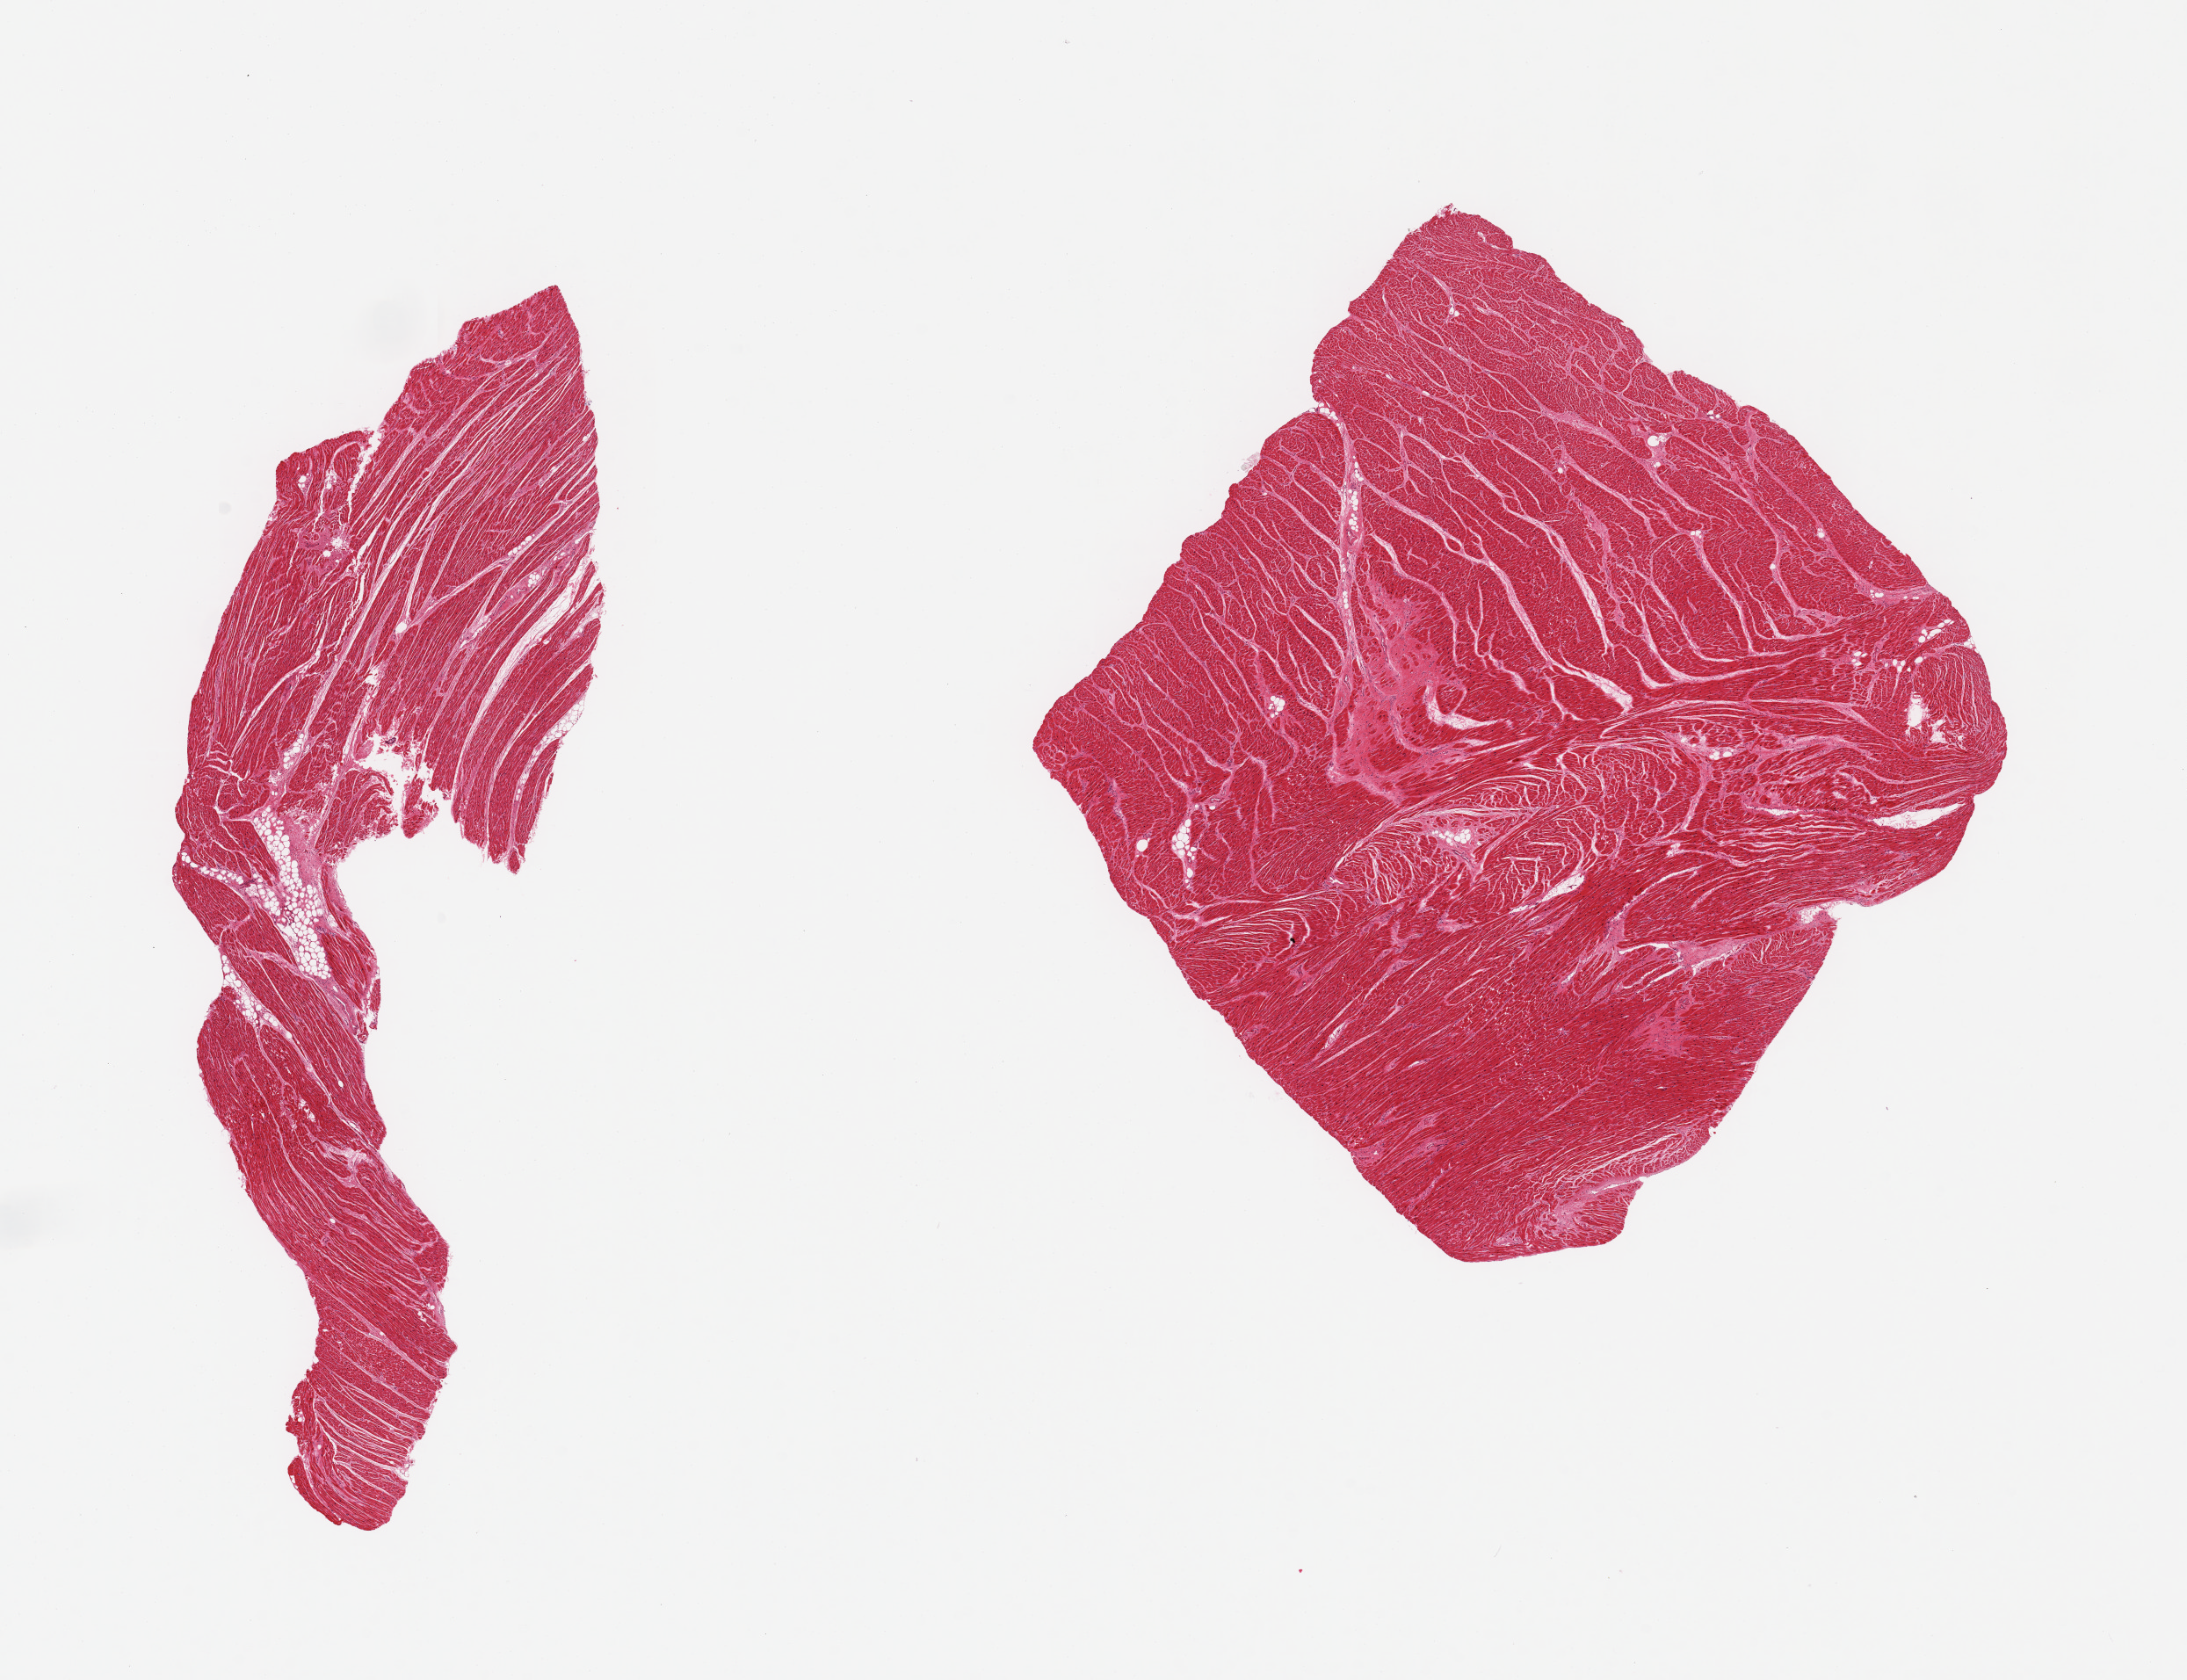
H&E whole-slide image, brightfield, shown as a low-resolution overview of the whole scanned area (about 19.7 x 15.1 mm, acquisition: 20x scan), PAXgene-fixed, paraffin-embedded tissue, target tissue: heart, donor tissue sample. Donor sex: male.
Review note (as recorded): 2 pieces; interstitial fibrosis and scarring, fatty degeneration.